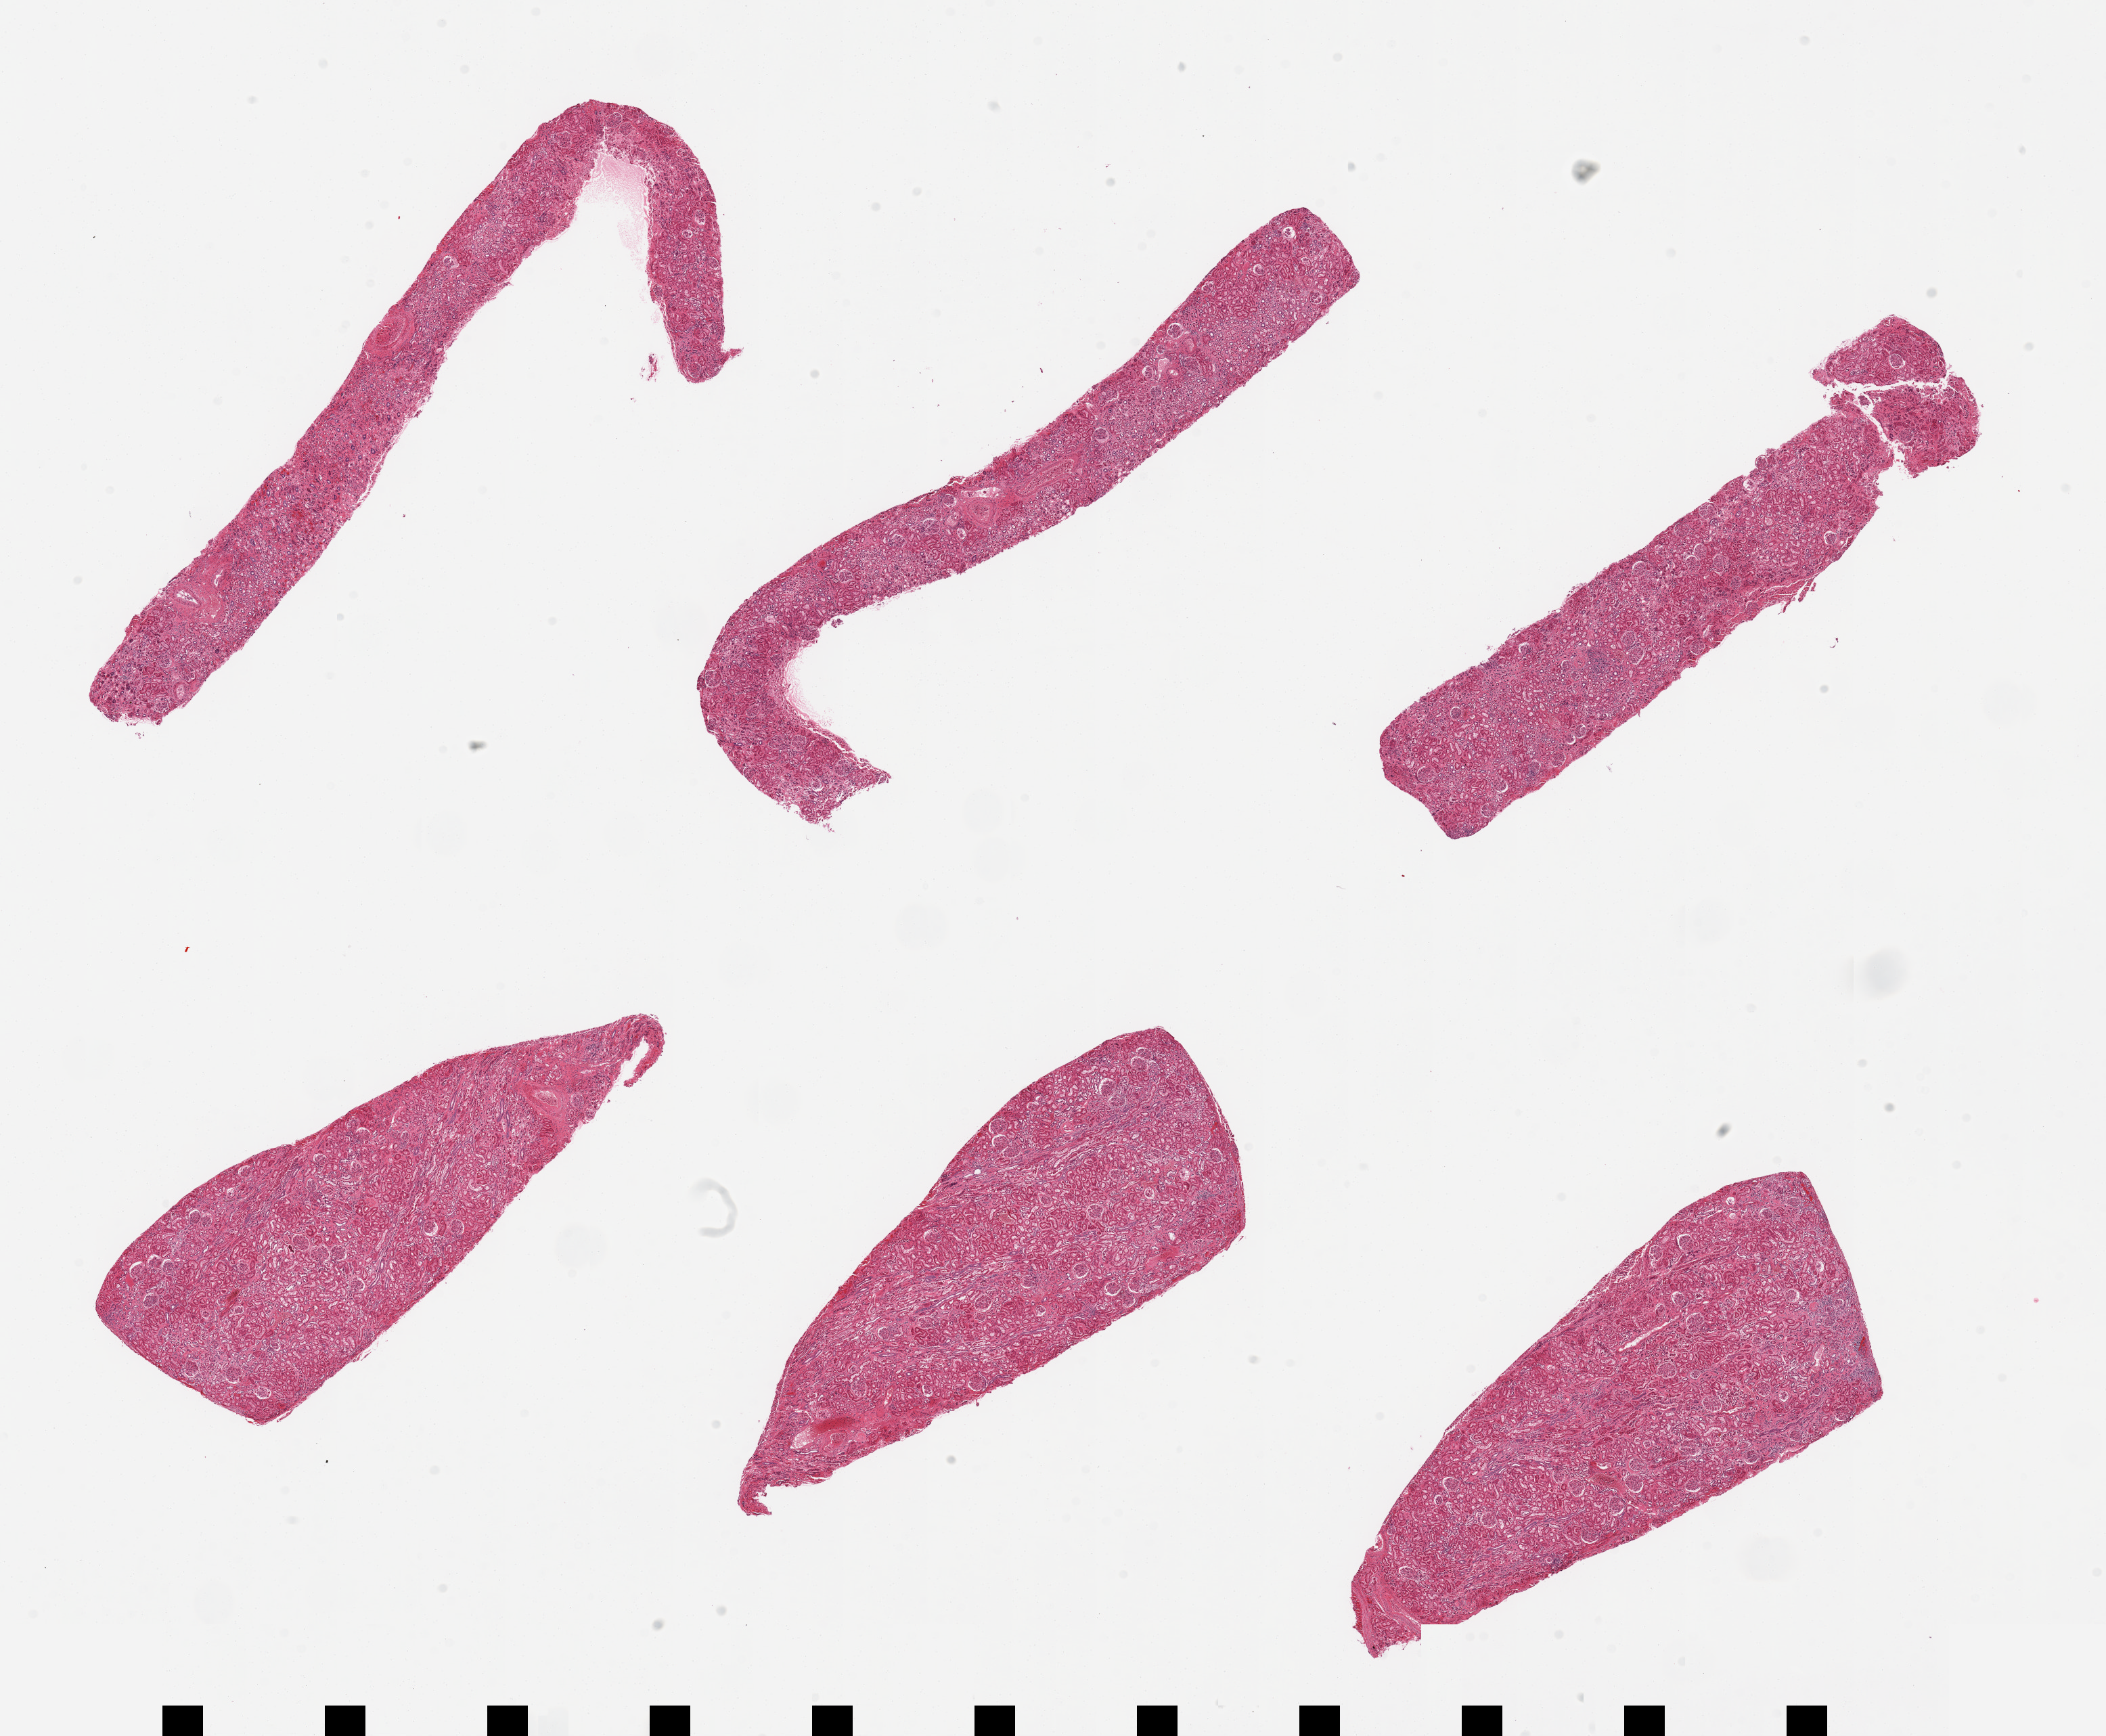
Digitized H&E-stained section — a low-resolution overview of the entire scanned area, about 24.6 x 20.3 mm, PAXgene-fixed paraffin-embedded (PFPE) section, section of renal cortex (target tissue), tissue donor sample. Donor sex: female.
Reviewer comment on this tissue sample: 6 pieces; mild patchy fibrosis.